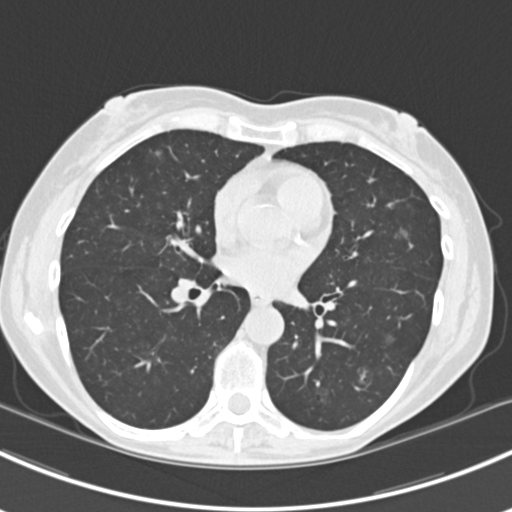
Chest CT (low-dose screening protocol), one axial image. Baseline screening round. Lung window (W 1500 / L -600 HU). 2 mm slice thickness. Standard (soft-tissue) reconstruction kernel (B30f). Female participant, aged 63 years at enrolment. Current smoker at enrolment.
- Expert-annotated lung lesion, bounding box (x1, y1, x2, y2) in pixels: (383, 217, 424, 254).
- The screening reader recorded 10 non-calcified nodules or masses ≥4 mm on this exam; which of them this box marks is not recorded.
- Official screen result: positive, change unspecified: nodule(s) >= 4 mm or enlarging nodule(s), mass(es), or other non-specific abnormalities suspicious for lung cancer.
- Later outcome: lung cancer diagnosed 751 days after this screen — bronchiolo-alveolar adenocarcinoma, NOS, right upper lobe, right middle lobe, right lower lobe, left upper lobe, left lower lobe, moderately differentiated (G2), stage IV (AJCC 6th edition).